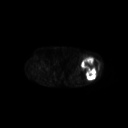
FDG PET of an extremity soft-tissue mass (from a PET/CT study), one axial slice; position 227 of 267 along the scan axis; 128 × 128 image matrix, field of view 700 × 700 mm. Patient: female, 62 years. Case-level facts recorded for this patient, not image findings: histological type: undifferentiated – high grade; grade: high; site of the primary tumour: left thigh.
Structures marked on this image (expert contour drawn on MRI and transferred to this co-registered scan by the dataset authors):
- gross tumour volume including surrounding oedema: bounding box (x1, y1, x2, y2) in pixels: (81, 56, 100, 80)
- gross tumour volume (mass): (81, 56, 99, 80)